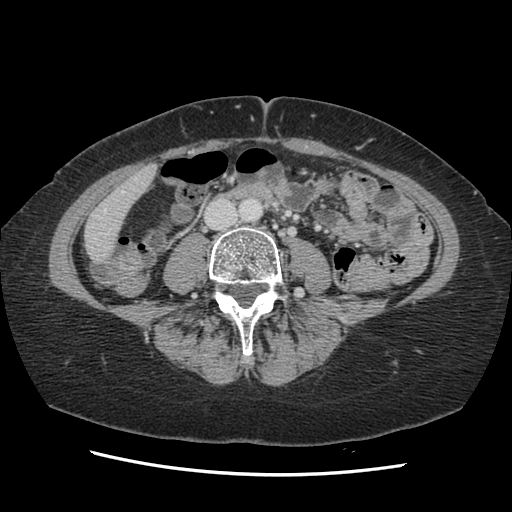
Contrast-enhanced abdominal CT, one axial slice. Slice 21 of 141 in the series (ordered by position). Soft-tissue window (W 400 / L 40 HU). 512 × 512 image matrix. Female patient, age 61 years. From the clinical record (not read from this slice): diagnosis: colorectal cancer liver metastases, imaged before liver resection; multiple liver metastases: no; largest metastasis: 2.4 cm; disease in both lobes: no.
Structures marked on this image (expert manual segmentation):
- hepatic veins: bounding box (x1, y1, x2, y2) in pixels: (104, 209, 107, 212)
- liver: (85, 167, 155, 260)
- planned liver remnant (the part of the liver to remain after resection): (85, 168, 155, 260)